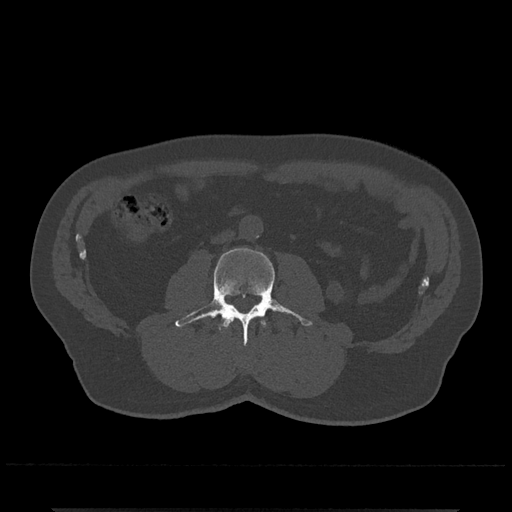
CT including the spine, one axial slice; position 224 of 797 along the scan axis; 120 kVp; bone window (W 1800 / L 400 HU); 0.5 mm slice thickness; 512 × 512 image matrix, field of view 393 × 393 mm. Male patient, age 67 years. From the clinical record (not read from this slice): primary cancer: prostate.
Structures marked on this image (semi-automatically segmented with operator editing):
- L2 vertebra: box from (x=220, y=318) to (x=265, y=331) px
- L3 vertebra: (x=175, y=248)–(x=313, y=345)